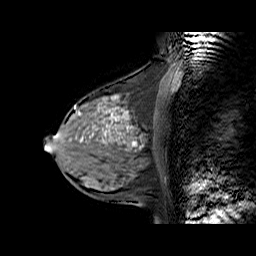
Breast MRI (dynamic contrast-enhanced), one sagittal slice; position 26 of 60 along the scan axis; dynamic contrast-enhanced series, time point 2 of 6 at this slice position (early post-contrast); 1.5 T; TE 6.3 ms, TR 32.9 ms; 4 mm slice thickness; 256 × 256 image matrix. Female patient. From the clinical record (not read from this slice): setting: breast cancer imaged before/during neoadjuvant chemotherapy; receptor status: HR-positive, HER2-negative.
Outlined on this slice (semi-automatically segmented with operator editing):
- analysis volume of interest (the breast-tissue region the enhancement analysis was run in; not a lesion): bounding box (x1, y1, x2, y2) in pixels: (57, 86, 169, 170)
- tumour enhancement mask (voxels above the 100 % enhancement threshold inside the analysis volume of interest): (81, 96, 136, 145)